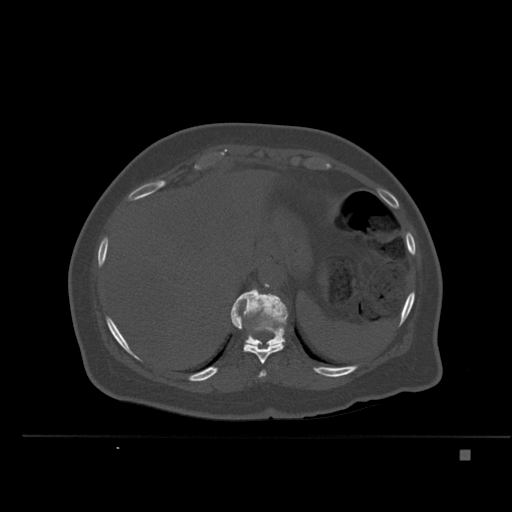
CT including the spine, one axial slice; slice 279 of 477 in the series (ordered by position); bone window (W 1800 / L 400 HU); 512 × 512 image matrix. Patient: female, 74 years. From the clinical record (not read from this slice): primary cancer: colon.
Annotated regions visible in this slice (semi-automatic segmentation, software-assisted and operator-edited):
- T10 vertebra: bounding box [x1, y1, x2, y2] px = [233, 314, 284, 364]
- T11 vertebra: [230, 288, 288, 346]
- T9 vertebra: [258, 370, 266, 378]